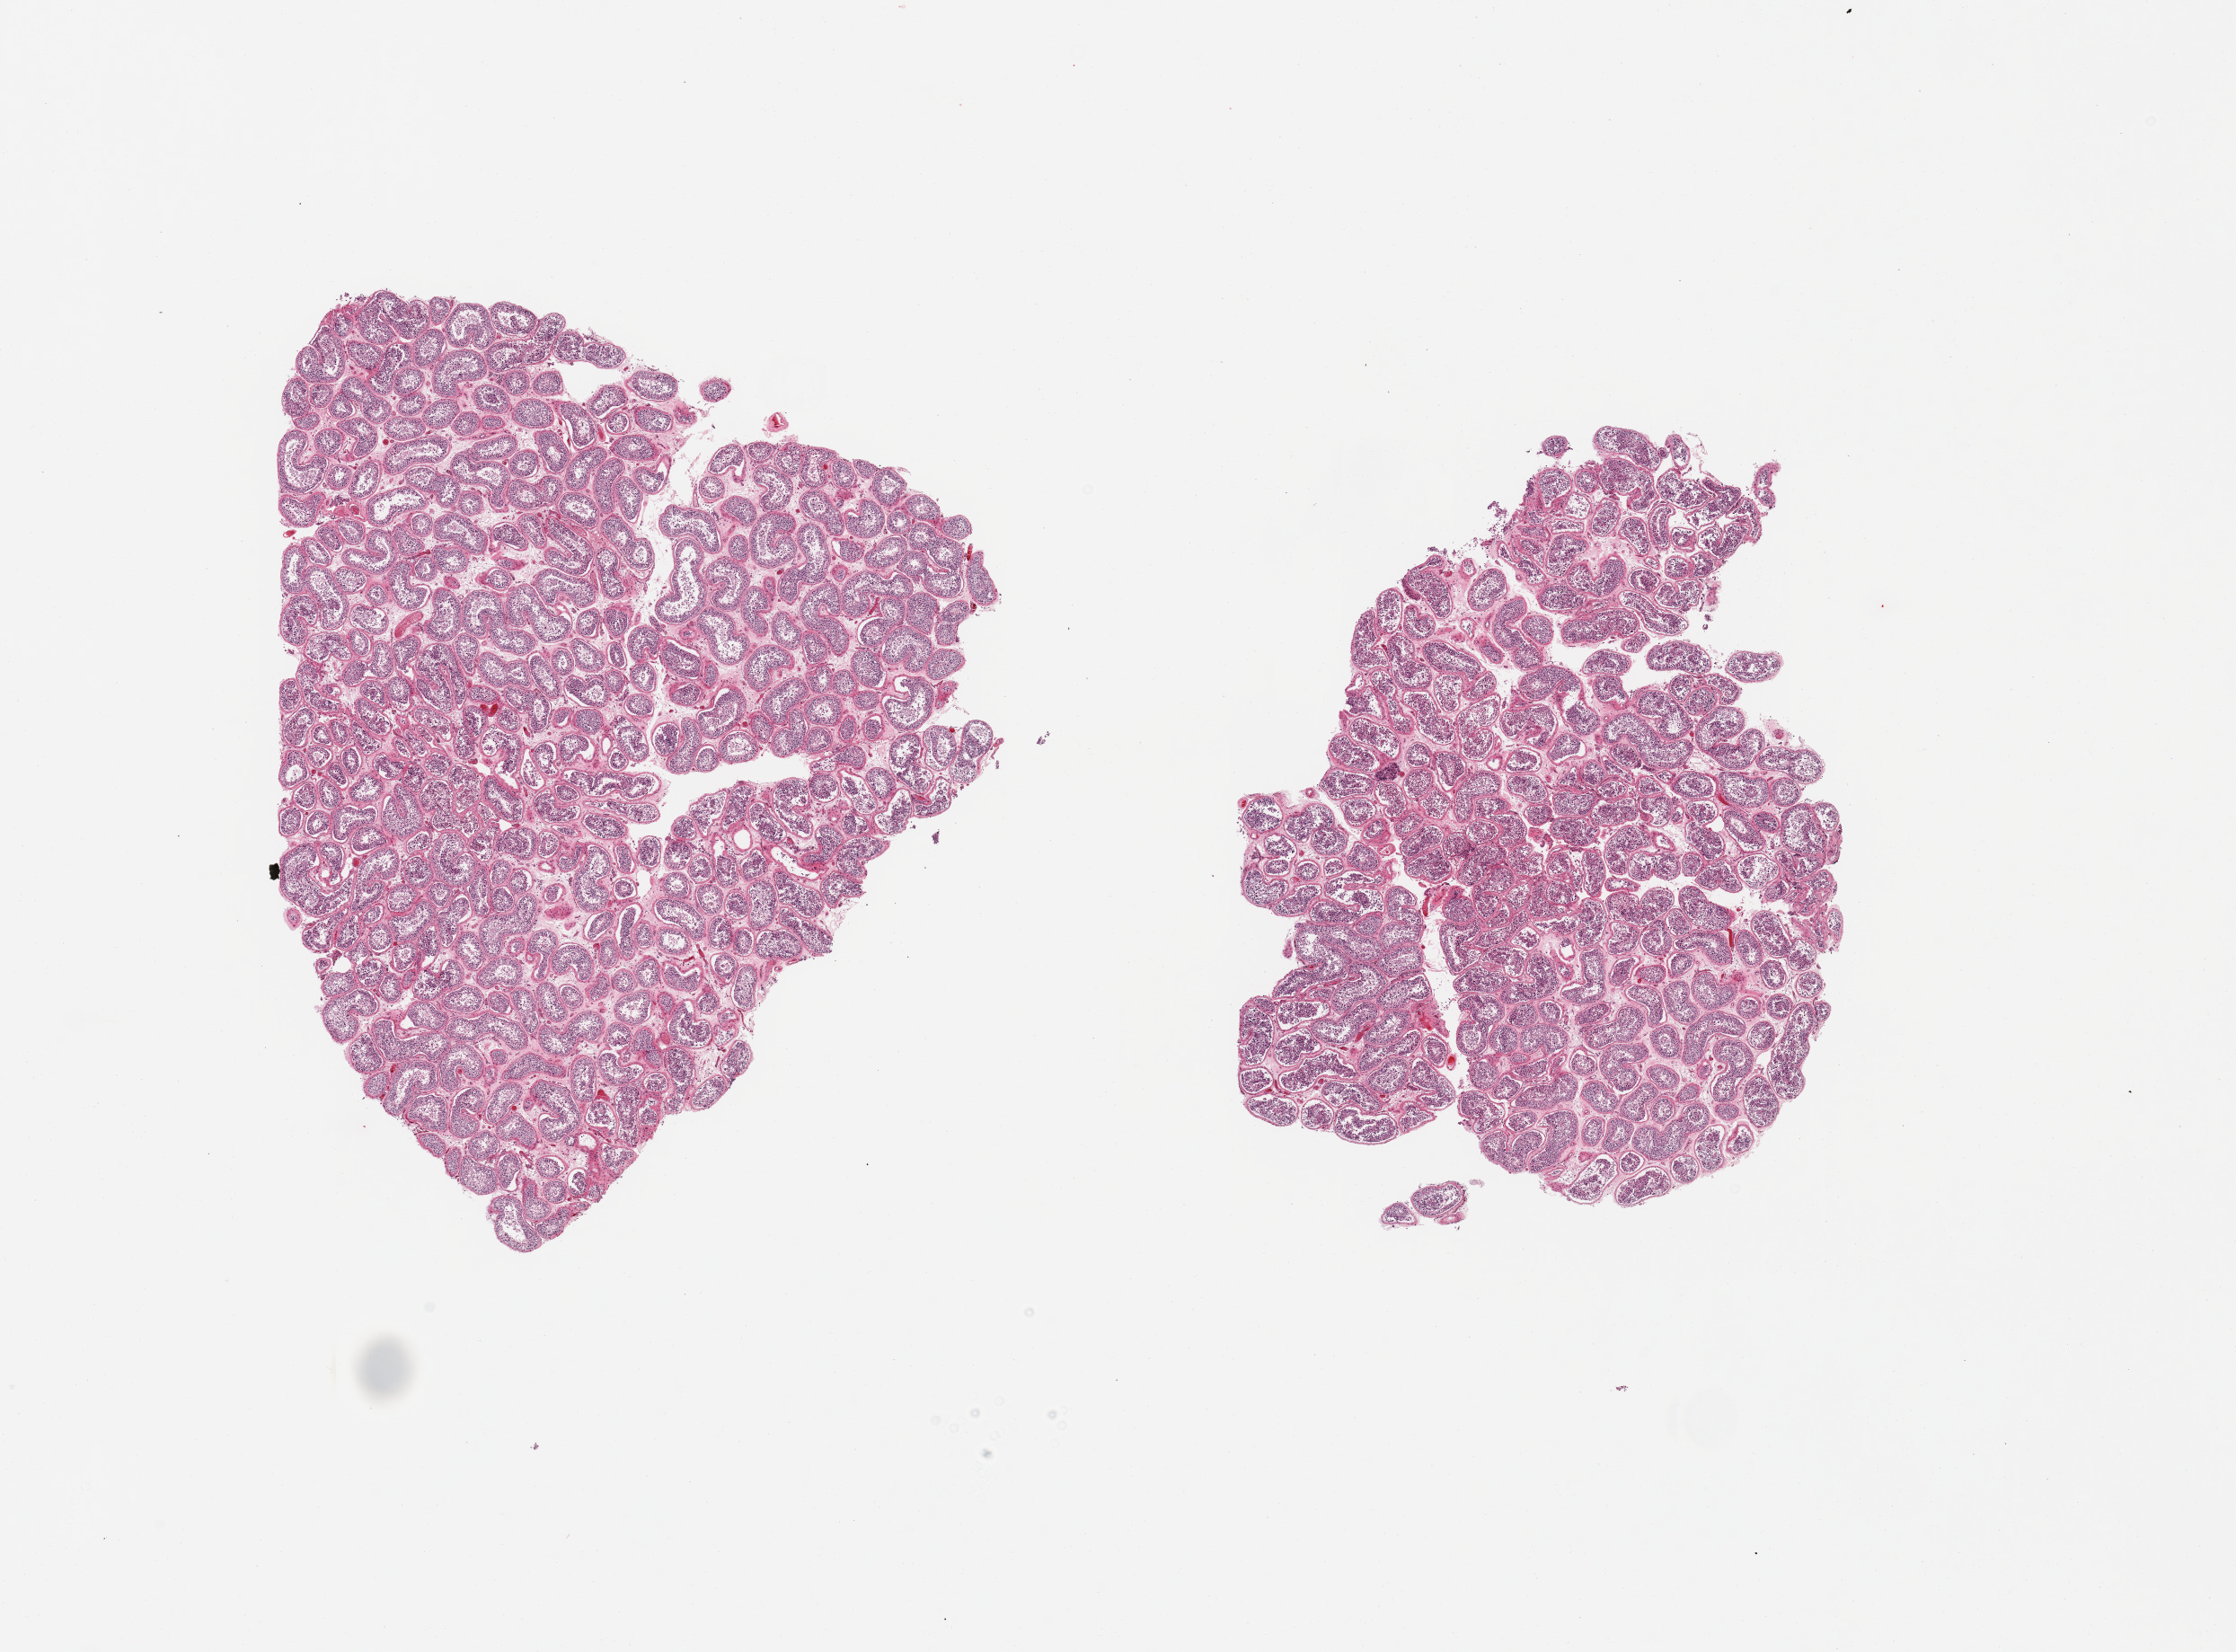
Whole-slide image, haematoxylin and eosin stain, brightfield, shown as a low-resolution overview of the whole scanned area (about 19.7 x 14.5 mm, from a 20x scan). PAXgene-fixed, paraffin-embedded tissue. Target tissue: testis. Tissue donor sample. Donor sex: male.
Reviewer comment on this tissue sample: 2 pieces; active spermatogenesis.